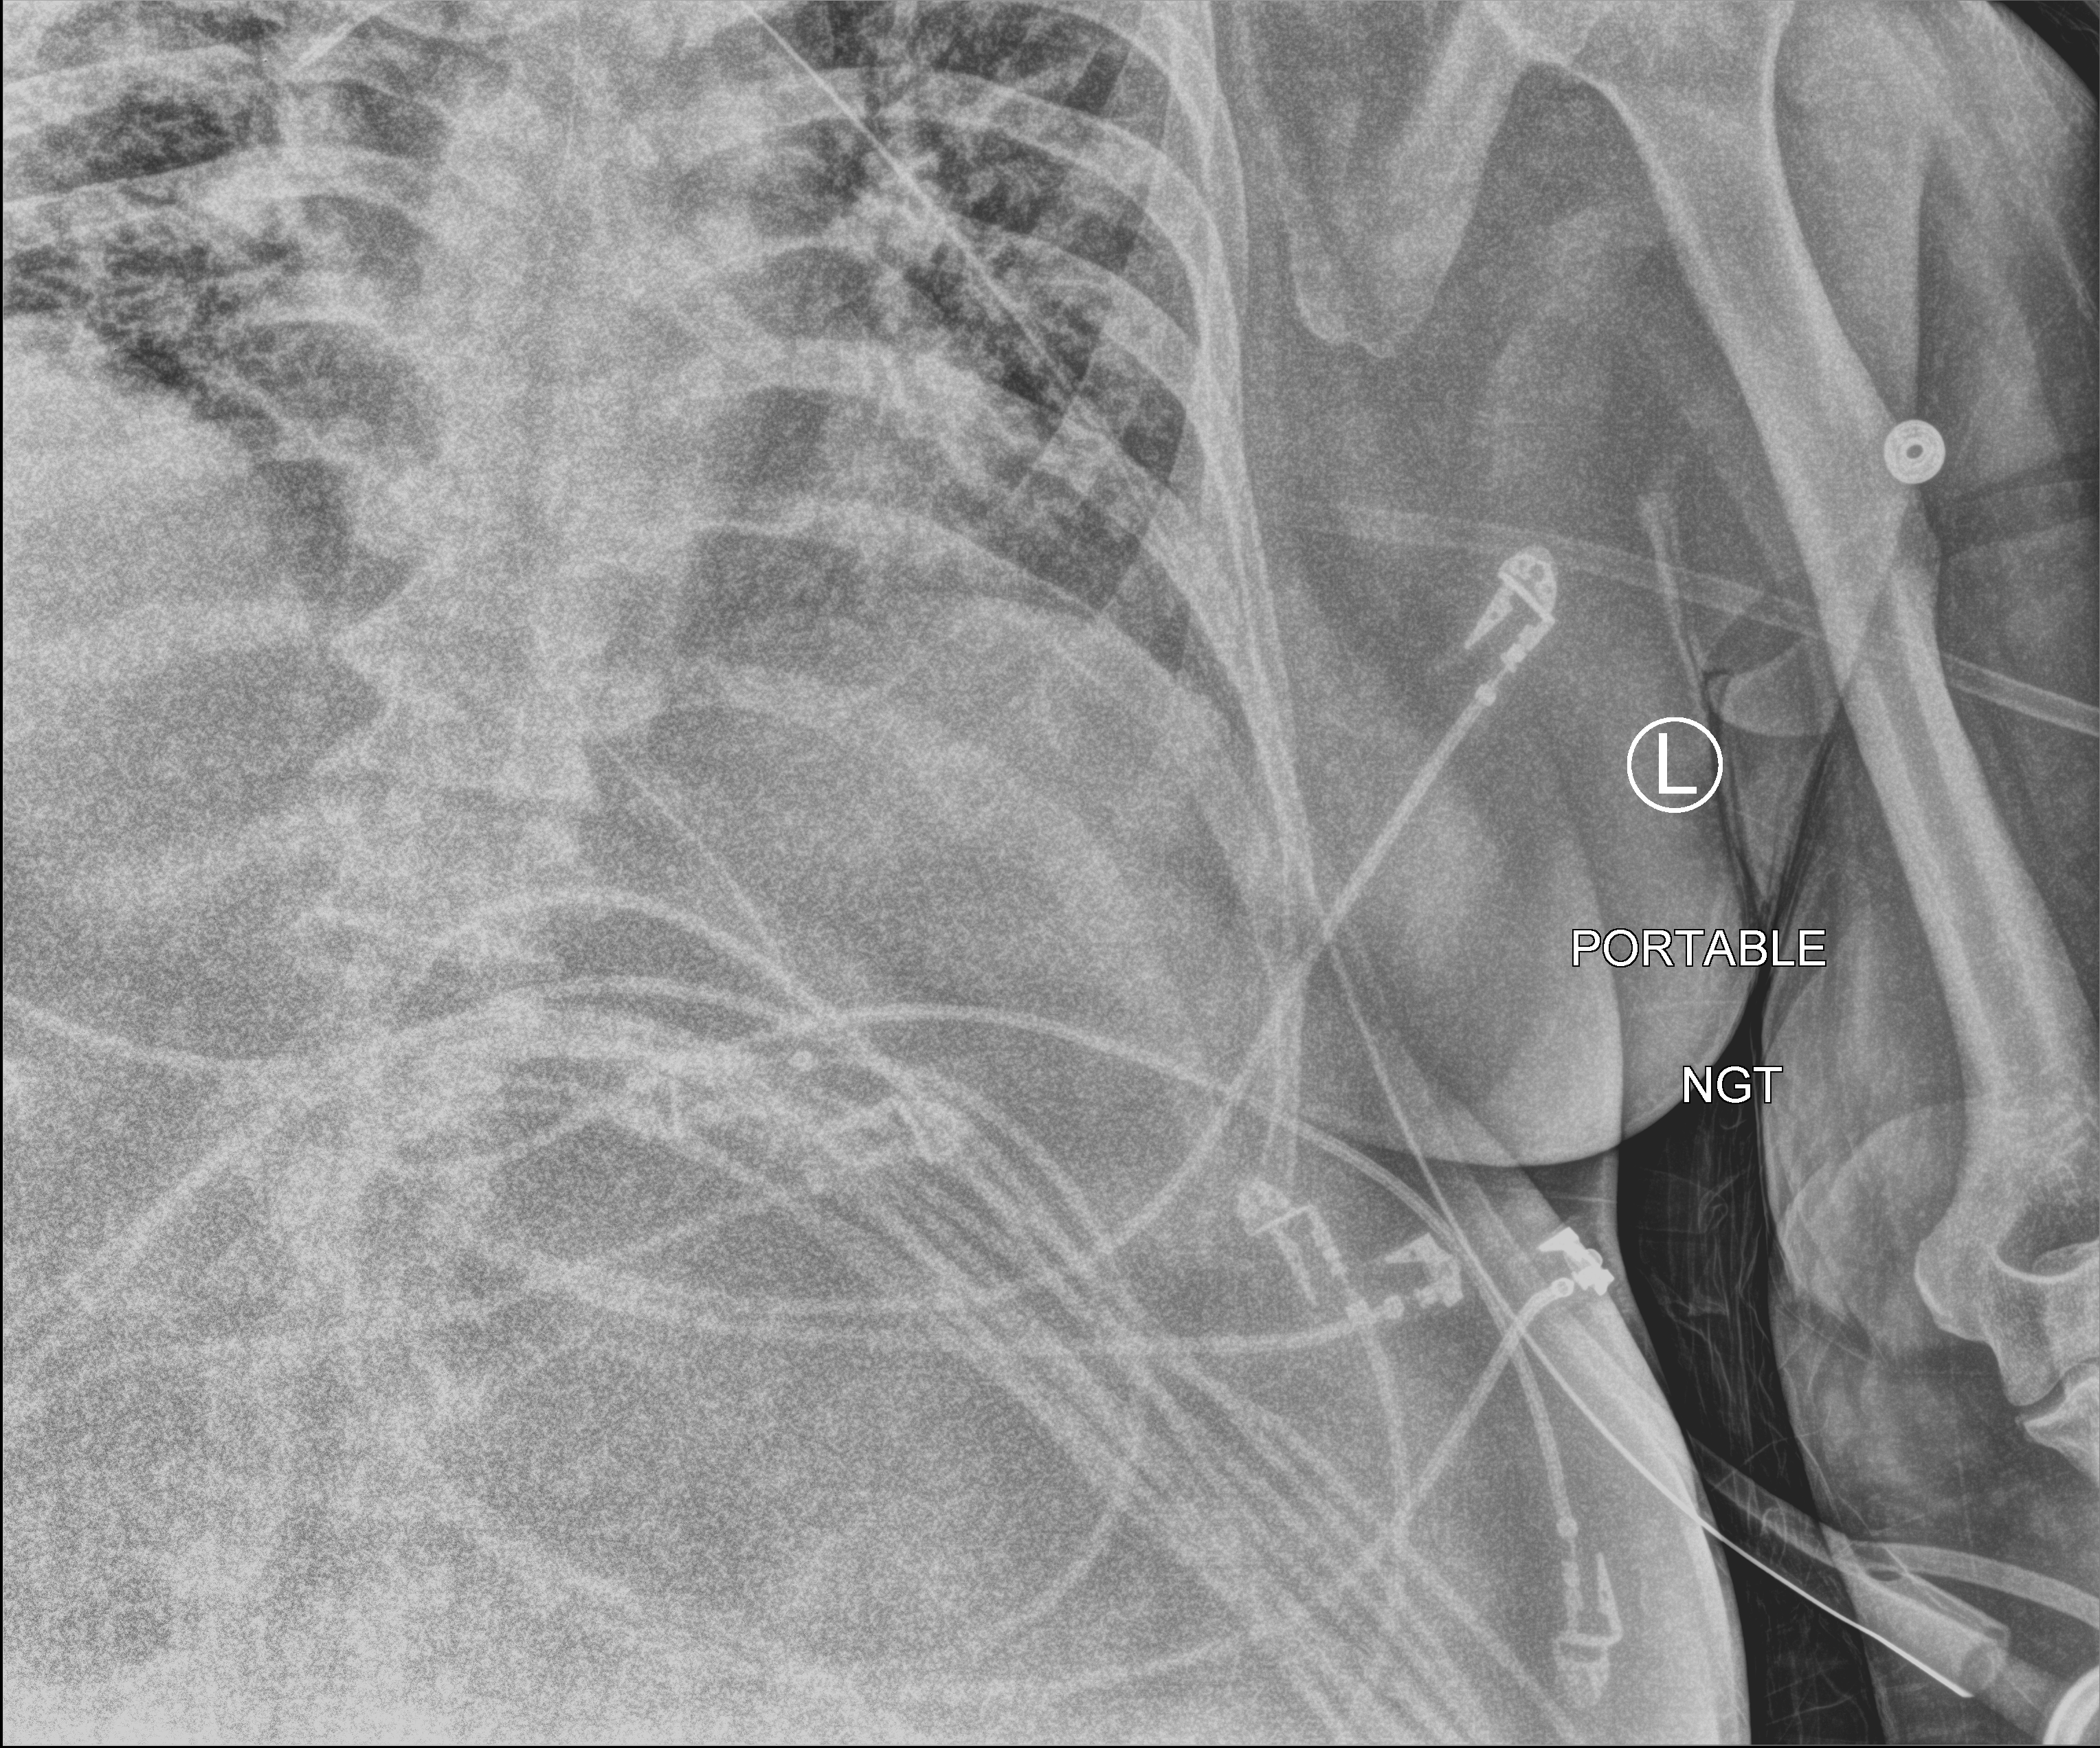
Portable chest radiograph, anteroposterior (AP) projection. Male patient hospitalised with COVID-19, age 18–59 years.
Admission-level facts for this patient (not findings on this image; timing relative to this image not recorded): diabetes (admission record): no.